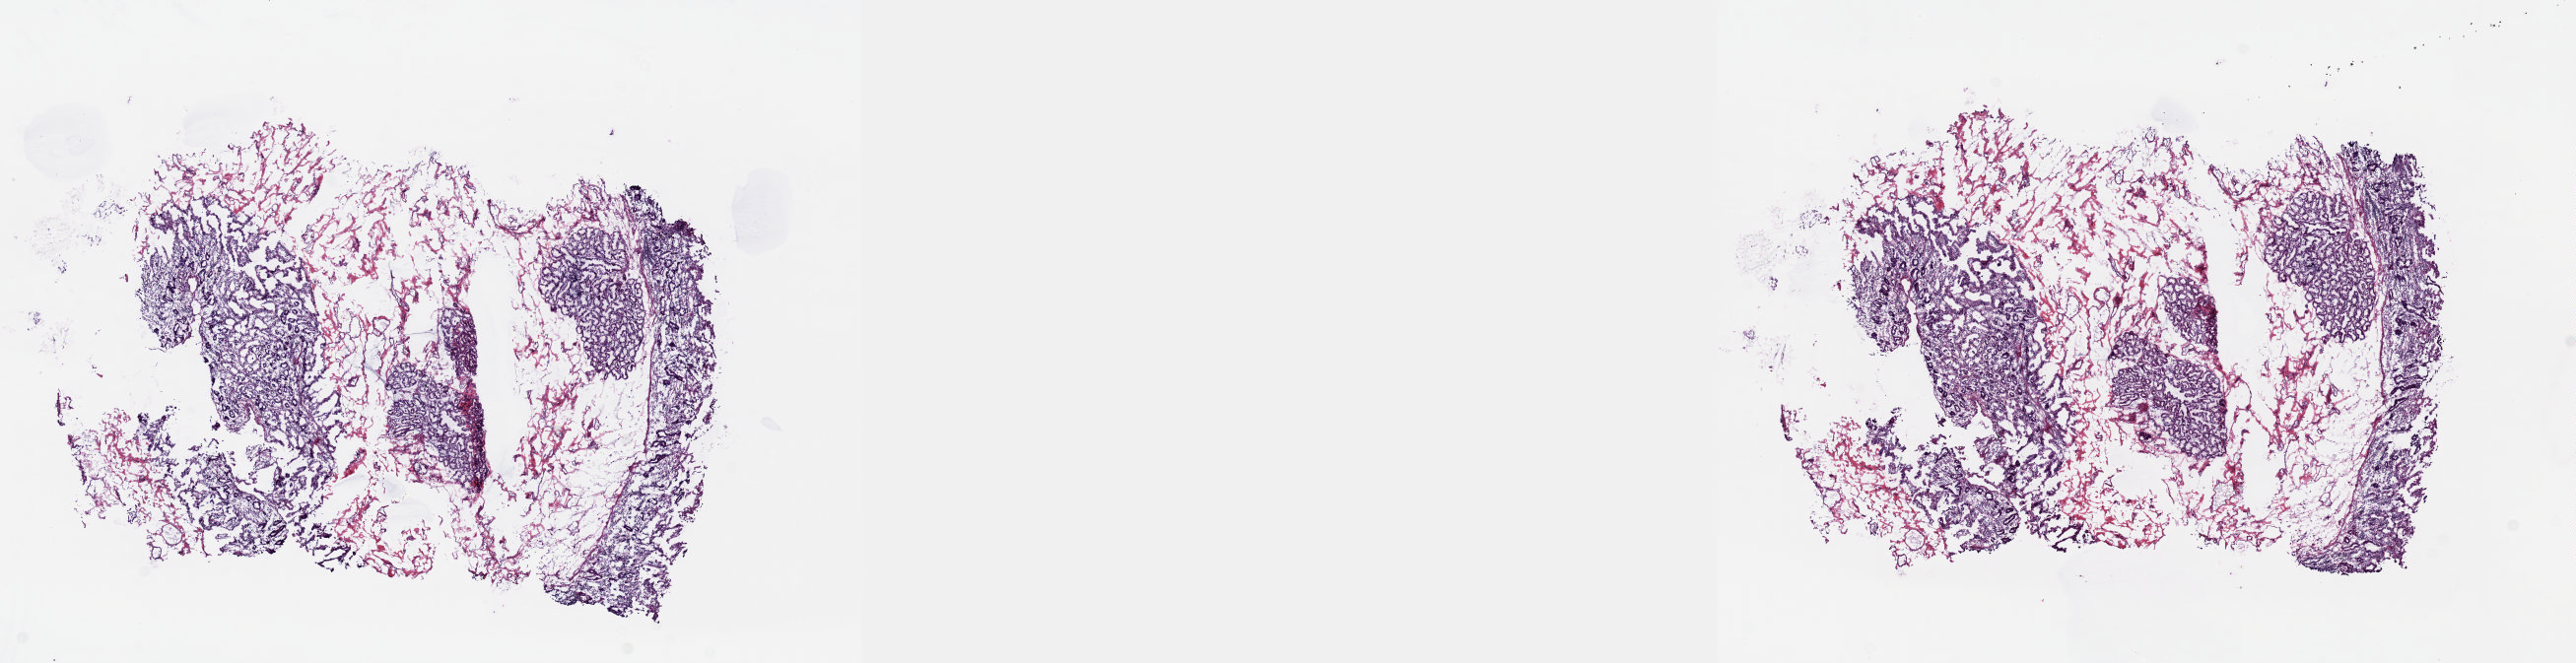
Digitized H&E-stained tissue section (whole slide) — whole scanned area (about 21.1 x 5.4 mm) shown as a low-resolution overview, frozen section, pancreas, solid tissue normal (non-tumour tissue) sample. Male patient; age at initial diagnosis 49 years. Composition of this section per pathologist review: tumour cells 0%, tumour nuclei 0%, normal cells 100%, stromal cells 0%, necrosis 0%. Inflammatory infiltration, as recorded: lymphocyte infiltration 3%, monocyte infiltration 0%, neutrophil infiltration 0%.
This section: solid tissue normal (non-tumour) sample from the same patient. Patient diagnosis: Infiltrating duct carcinoma, NOS.